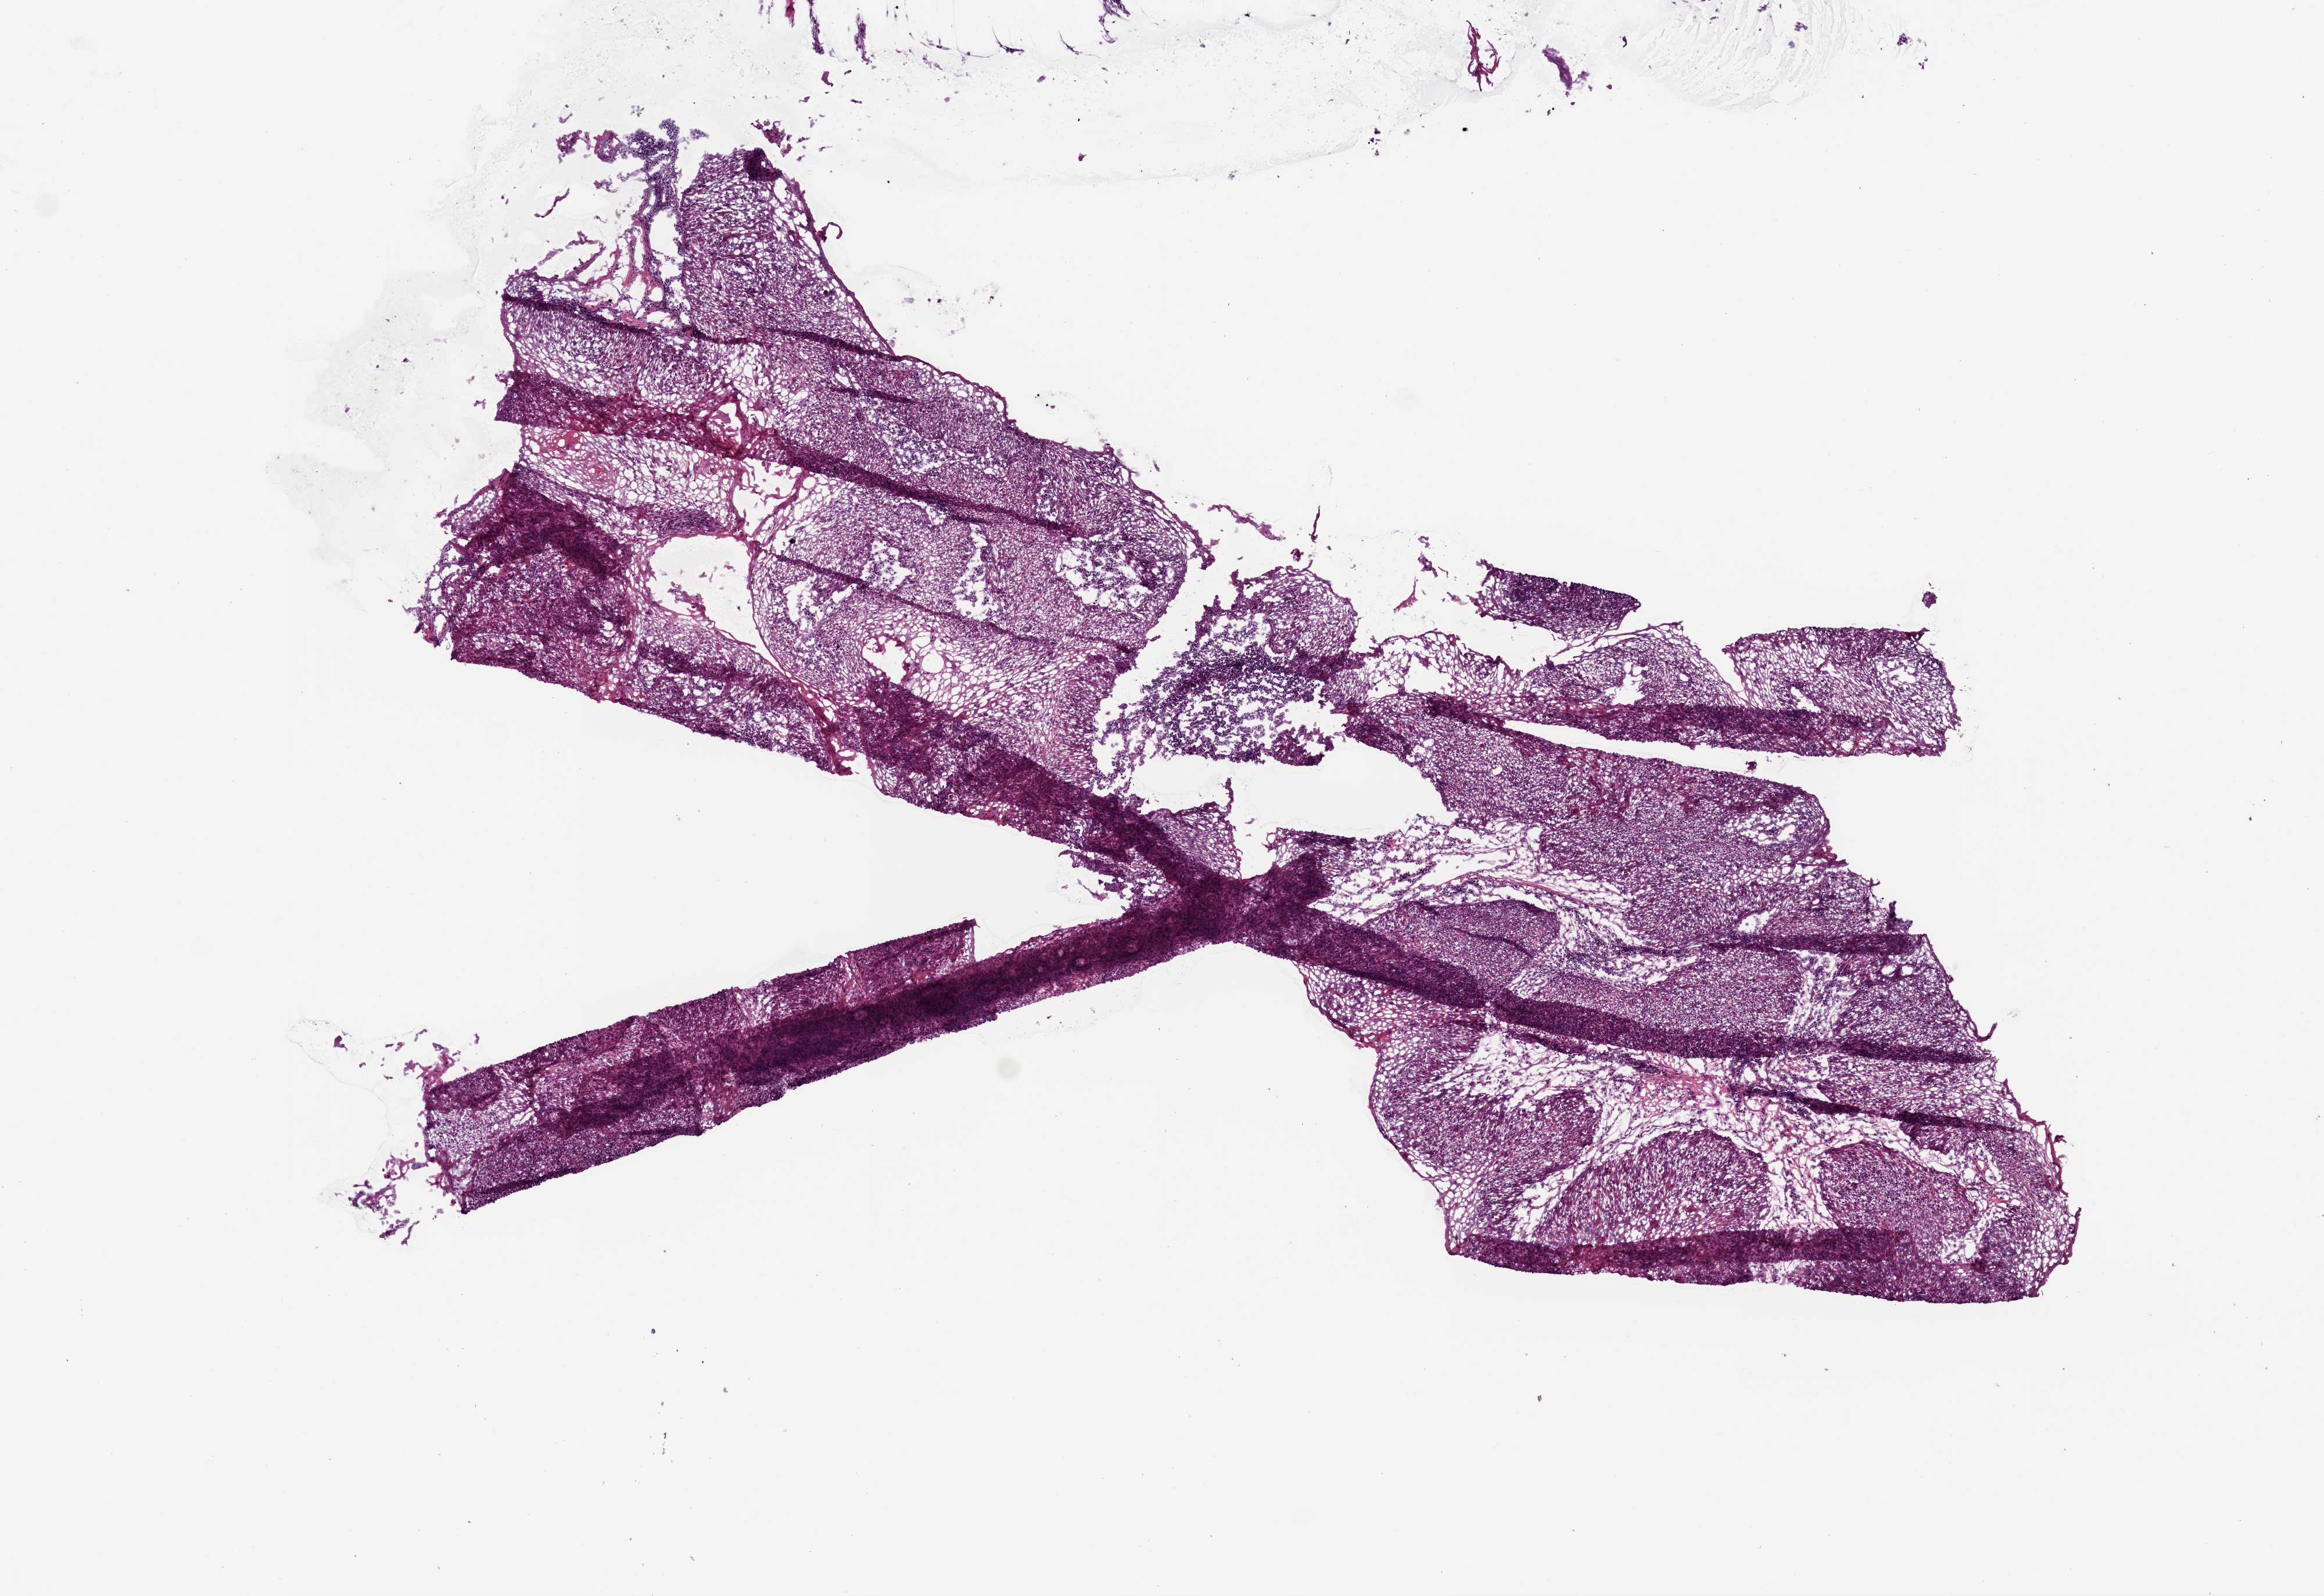
H&E whole-slide image — a low-resolution overview of the entire scanned area, about 8.0 x 5.5 mm. Frozen section from the bottom of the tissue portion. Head and neck, primary tumour sample. Female patient; age at initial diagnosis 76 years. Histologic grade: G3 (poorly differentiated). Slide review estimates, as recorded: tumour cells 0%, tumour nuclei 0%, normal cells 0%, stromal cells 0%, necrosis 0%.
- histologic diagnosis: Squamous cell carcinoma, NOS (hard palate)
- AJCC pathologic stage: IVA (7th edition)
- TNM: T4a N2b